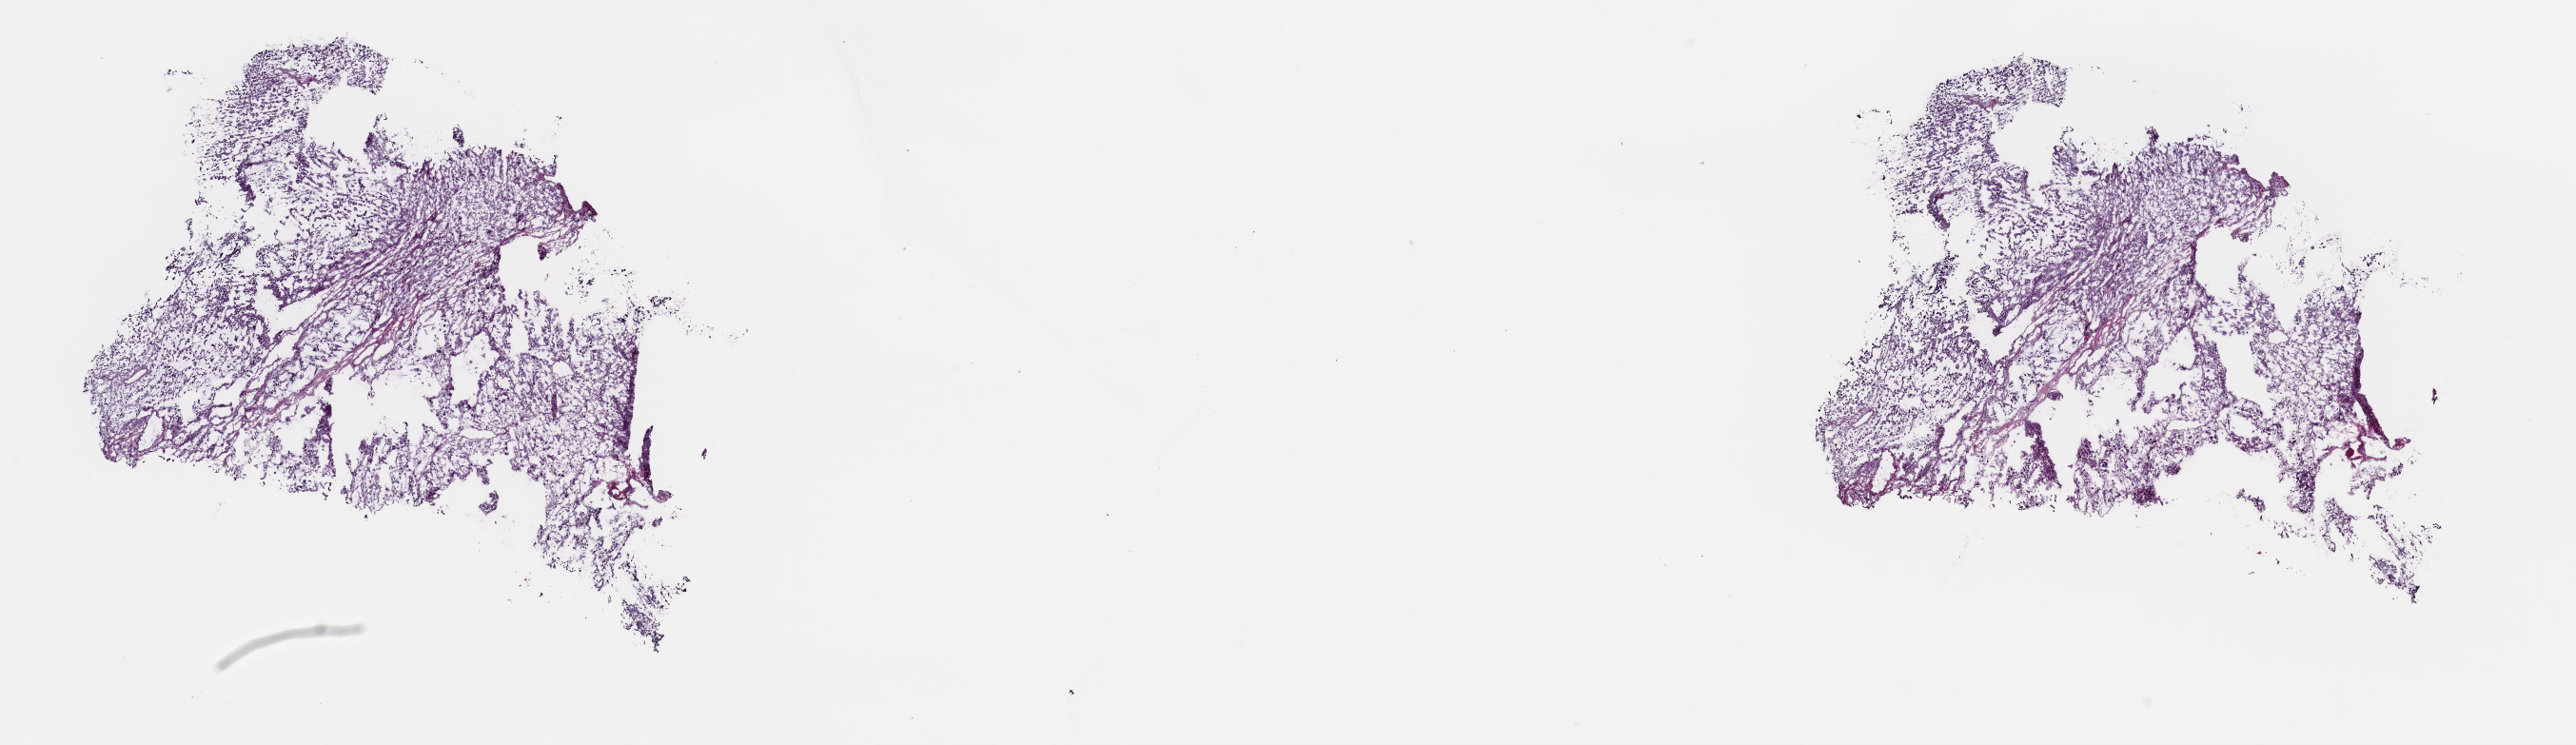
Whole-slide histology image, H&E-stained, low-resolution overview of the scanned area, about 21.4 x 6.2 mm; frozen section from the top of the tissue portion; primary tumour sample from the adrenal cortex. Female patient; age at initial diagnosis 26 years. Composition of this section per pathologist review: tumour cells 100%, tumour nuclei 95%, normal cells 0%, stromal cells 0%, necrosis 0%. Inflammatory infiltration, as recorded: lymphocyte infiltration 0%, monocyte infiltration 0%, neutrophil infiltration 0%.
Pathologic diagnosis: Adrenal cortical carcinoma. Laterality: right.